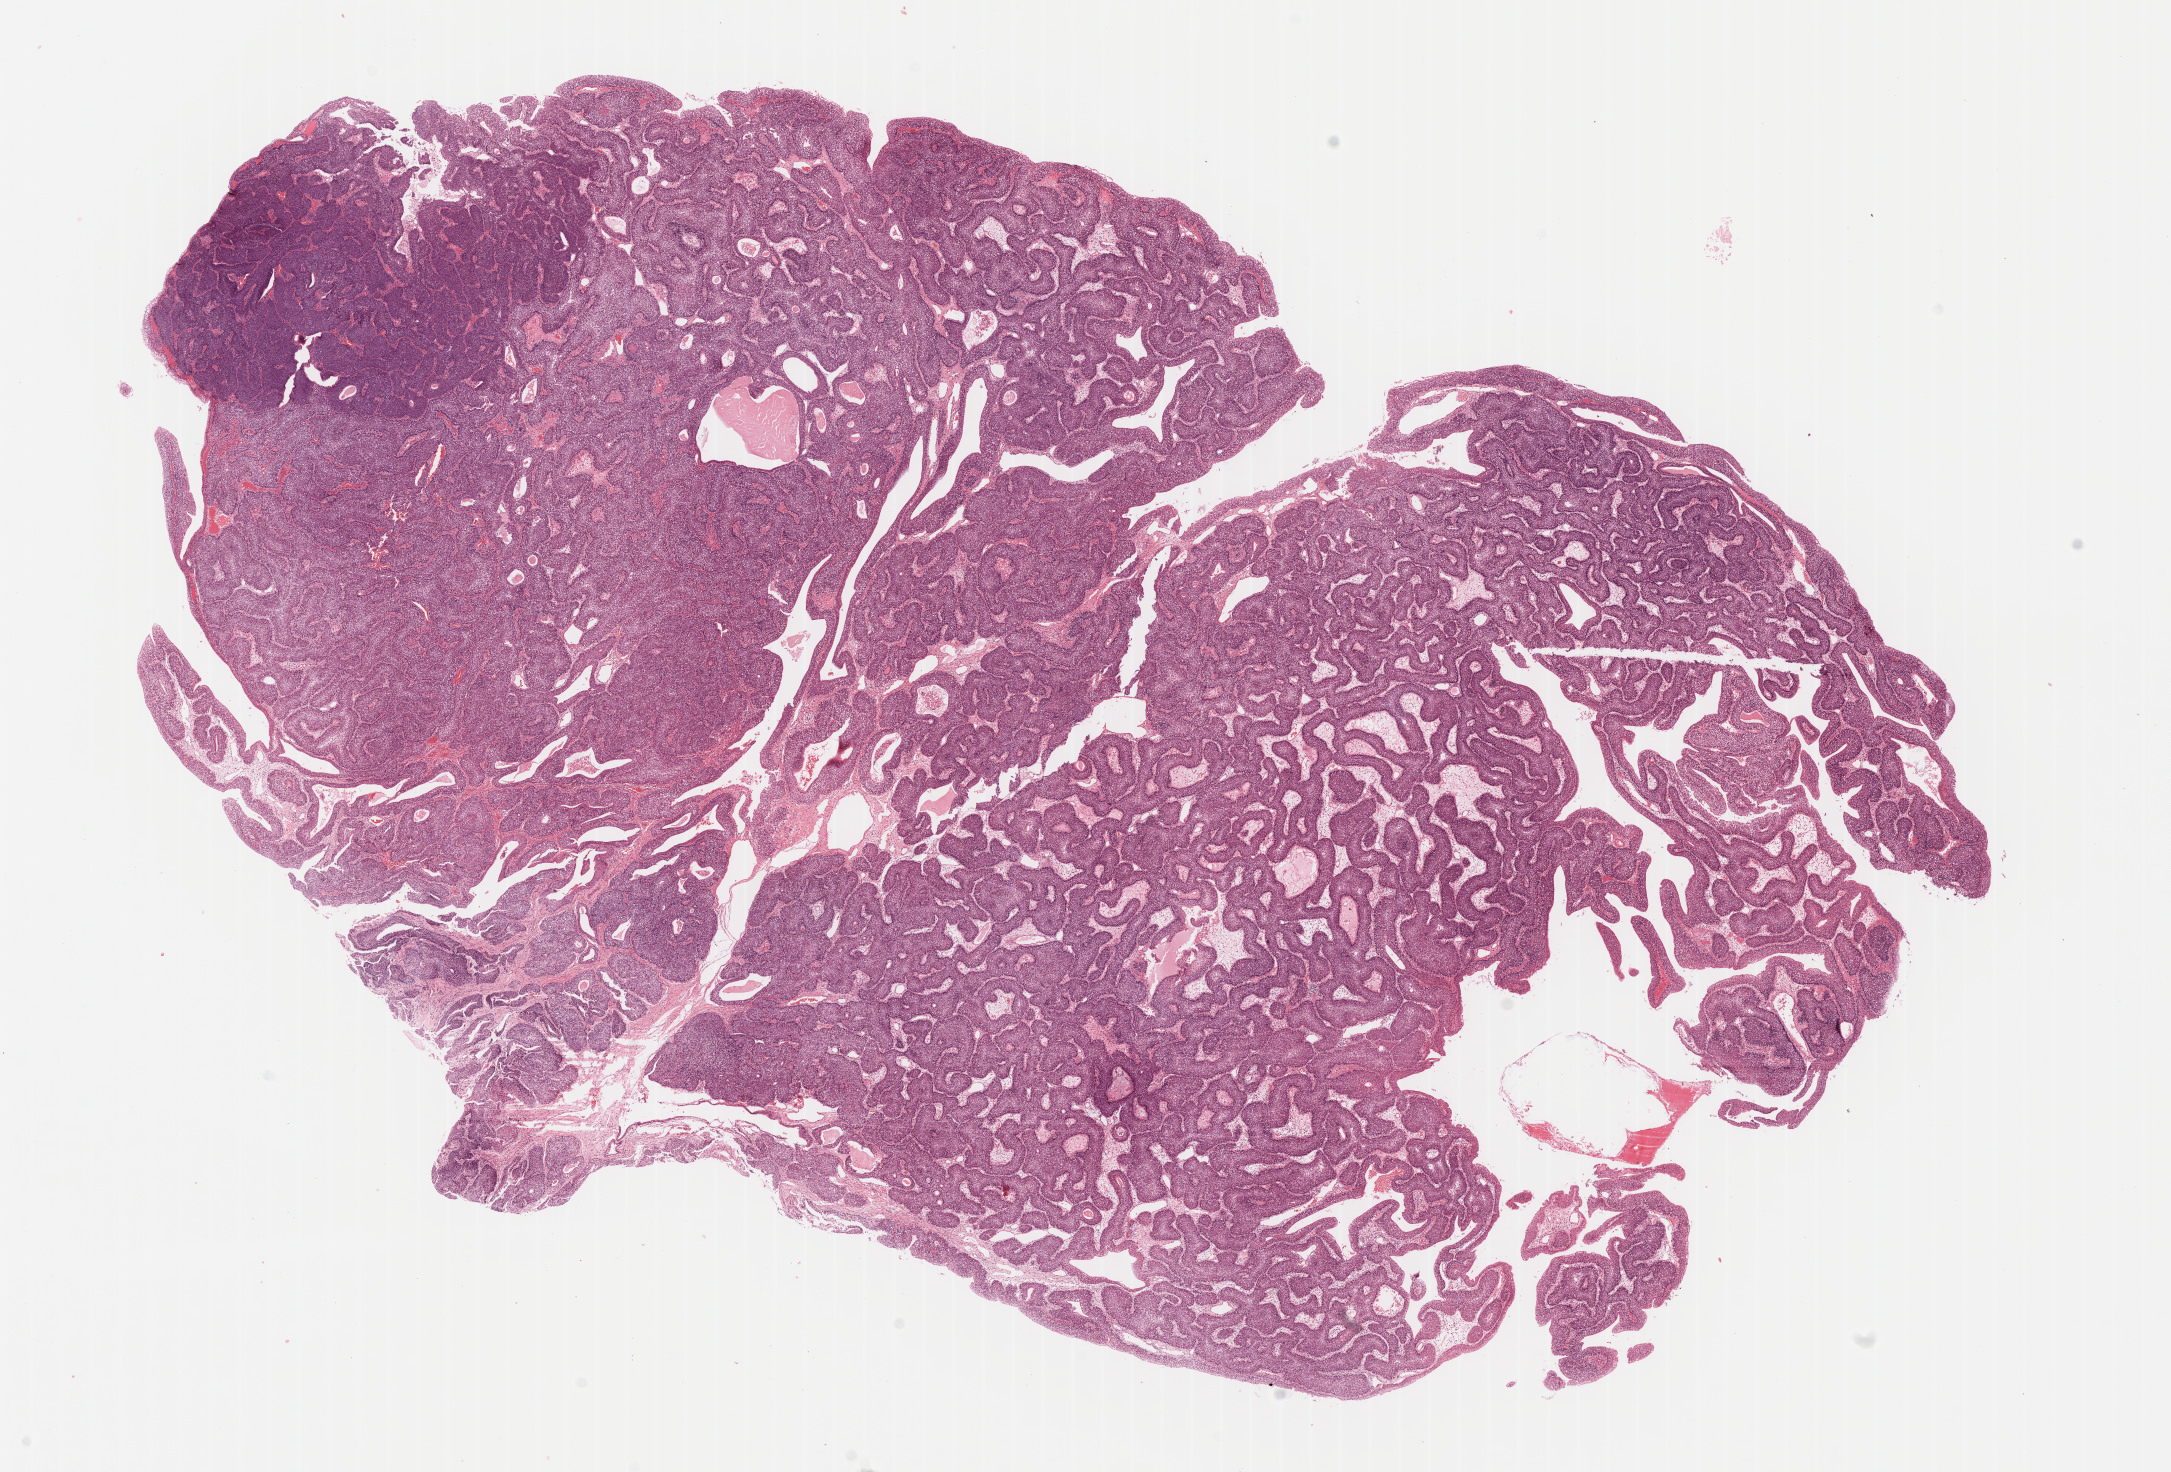
H&E whole-slide image, whole scanned area (about 17.1 x 11.6 mm) shown as a low-resolution overview. Formalin-fixed paraffin-embedded (FFPE) diagnostic section. Primary tumour sample from the bladder. Patient: male, age at initial diagnosis 37 years. Histologic grade: low grade.
Histologic diagnosis: Papillary transitional cell carcinoma. AJCC pathologic stage: II (7th edition).